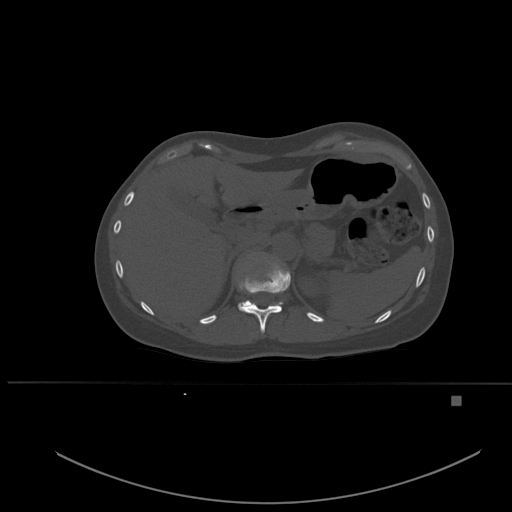
CT including the spine, one axial slice; position 267 of 651 along the scan axis; bone window (W 1800 / L 400 HU); 1.5 mm slice thickness; 512 × 512 image matrix, field of view 443 × 443 mm. Patient: female, 49 years. From the clinical record (not read from this slice): primary cancer: breast; vertebrae with lytic lesions (as recorded): L3, T12, L4.
Annotated regions visible in this slice (semi-automatically segmented with operator editing):
- T11 vertebra: bounding box (x1, y1, x2, y2) in pixels: (238, 263, 291, 334)
- T12 vertebra: (238, 292, 283, 308)